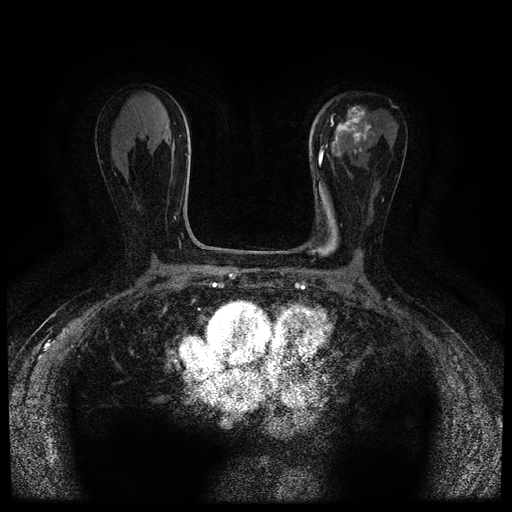
Breast MRI (dynamic contrast-enhanced, multi-phase), one axial slice. Position 44 of 116 along the scan axis. Dynamic contrast-enhanced series, time point 2 of 5 at this slice position (early post-contrast). 1.5 T. TE 2.7 ms, TR 5.4 ms. 2 mm slice thickness. 512 × 512 image matrix, field of view 320 × 320 mm. Patient: female, 80 years.
Annotated regions visible in this slice (semi-automatic segmentation, software-assisted and operator-edited):
- breast lesion (labelled 'tumour' in the annotation; benign lesions carry a separate 'benign' label): bounding box <327,104,375,156> (left, top, right, bottom; pixels)